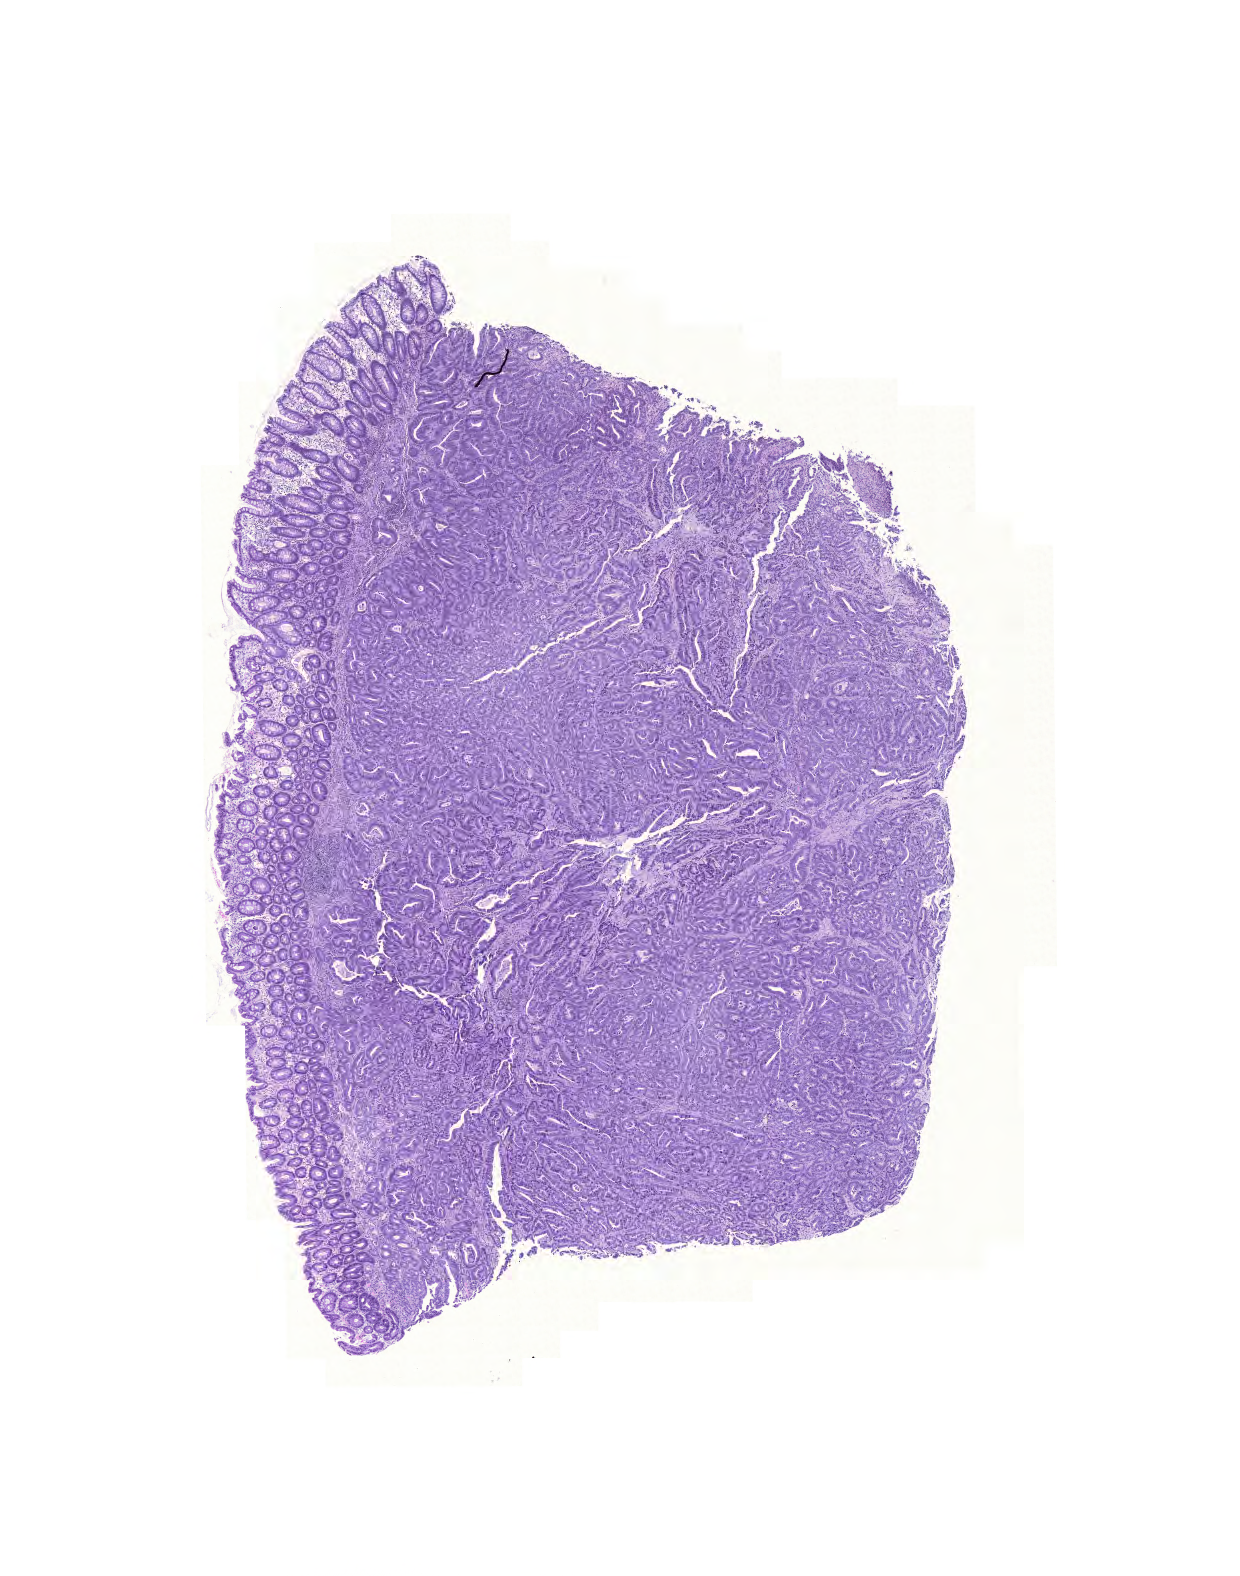
Whole-slide histology image, Hematoxylin and eosin (H&E) stained — a low-resolution overview of the entire scanned area, about 9.2 x 11.7 mm; formalin-fixed paraffin-embedded (FFPE) diagnostic section; primary tumour sample from the colon. Patient: female, age at initial diagnosis 86 years.
Pathologic diagnosis: Adenocarcinoma, NOS (ascending colon).